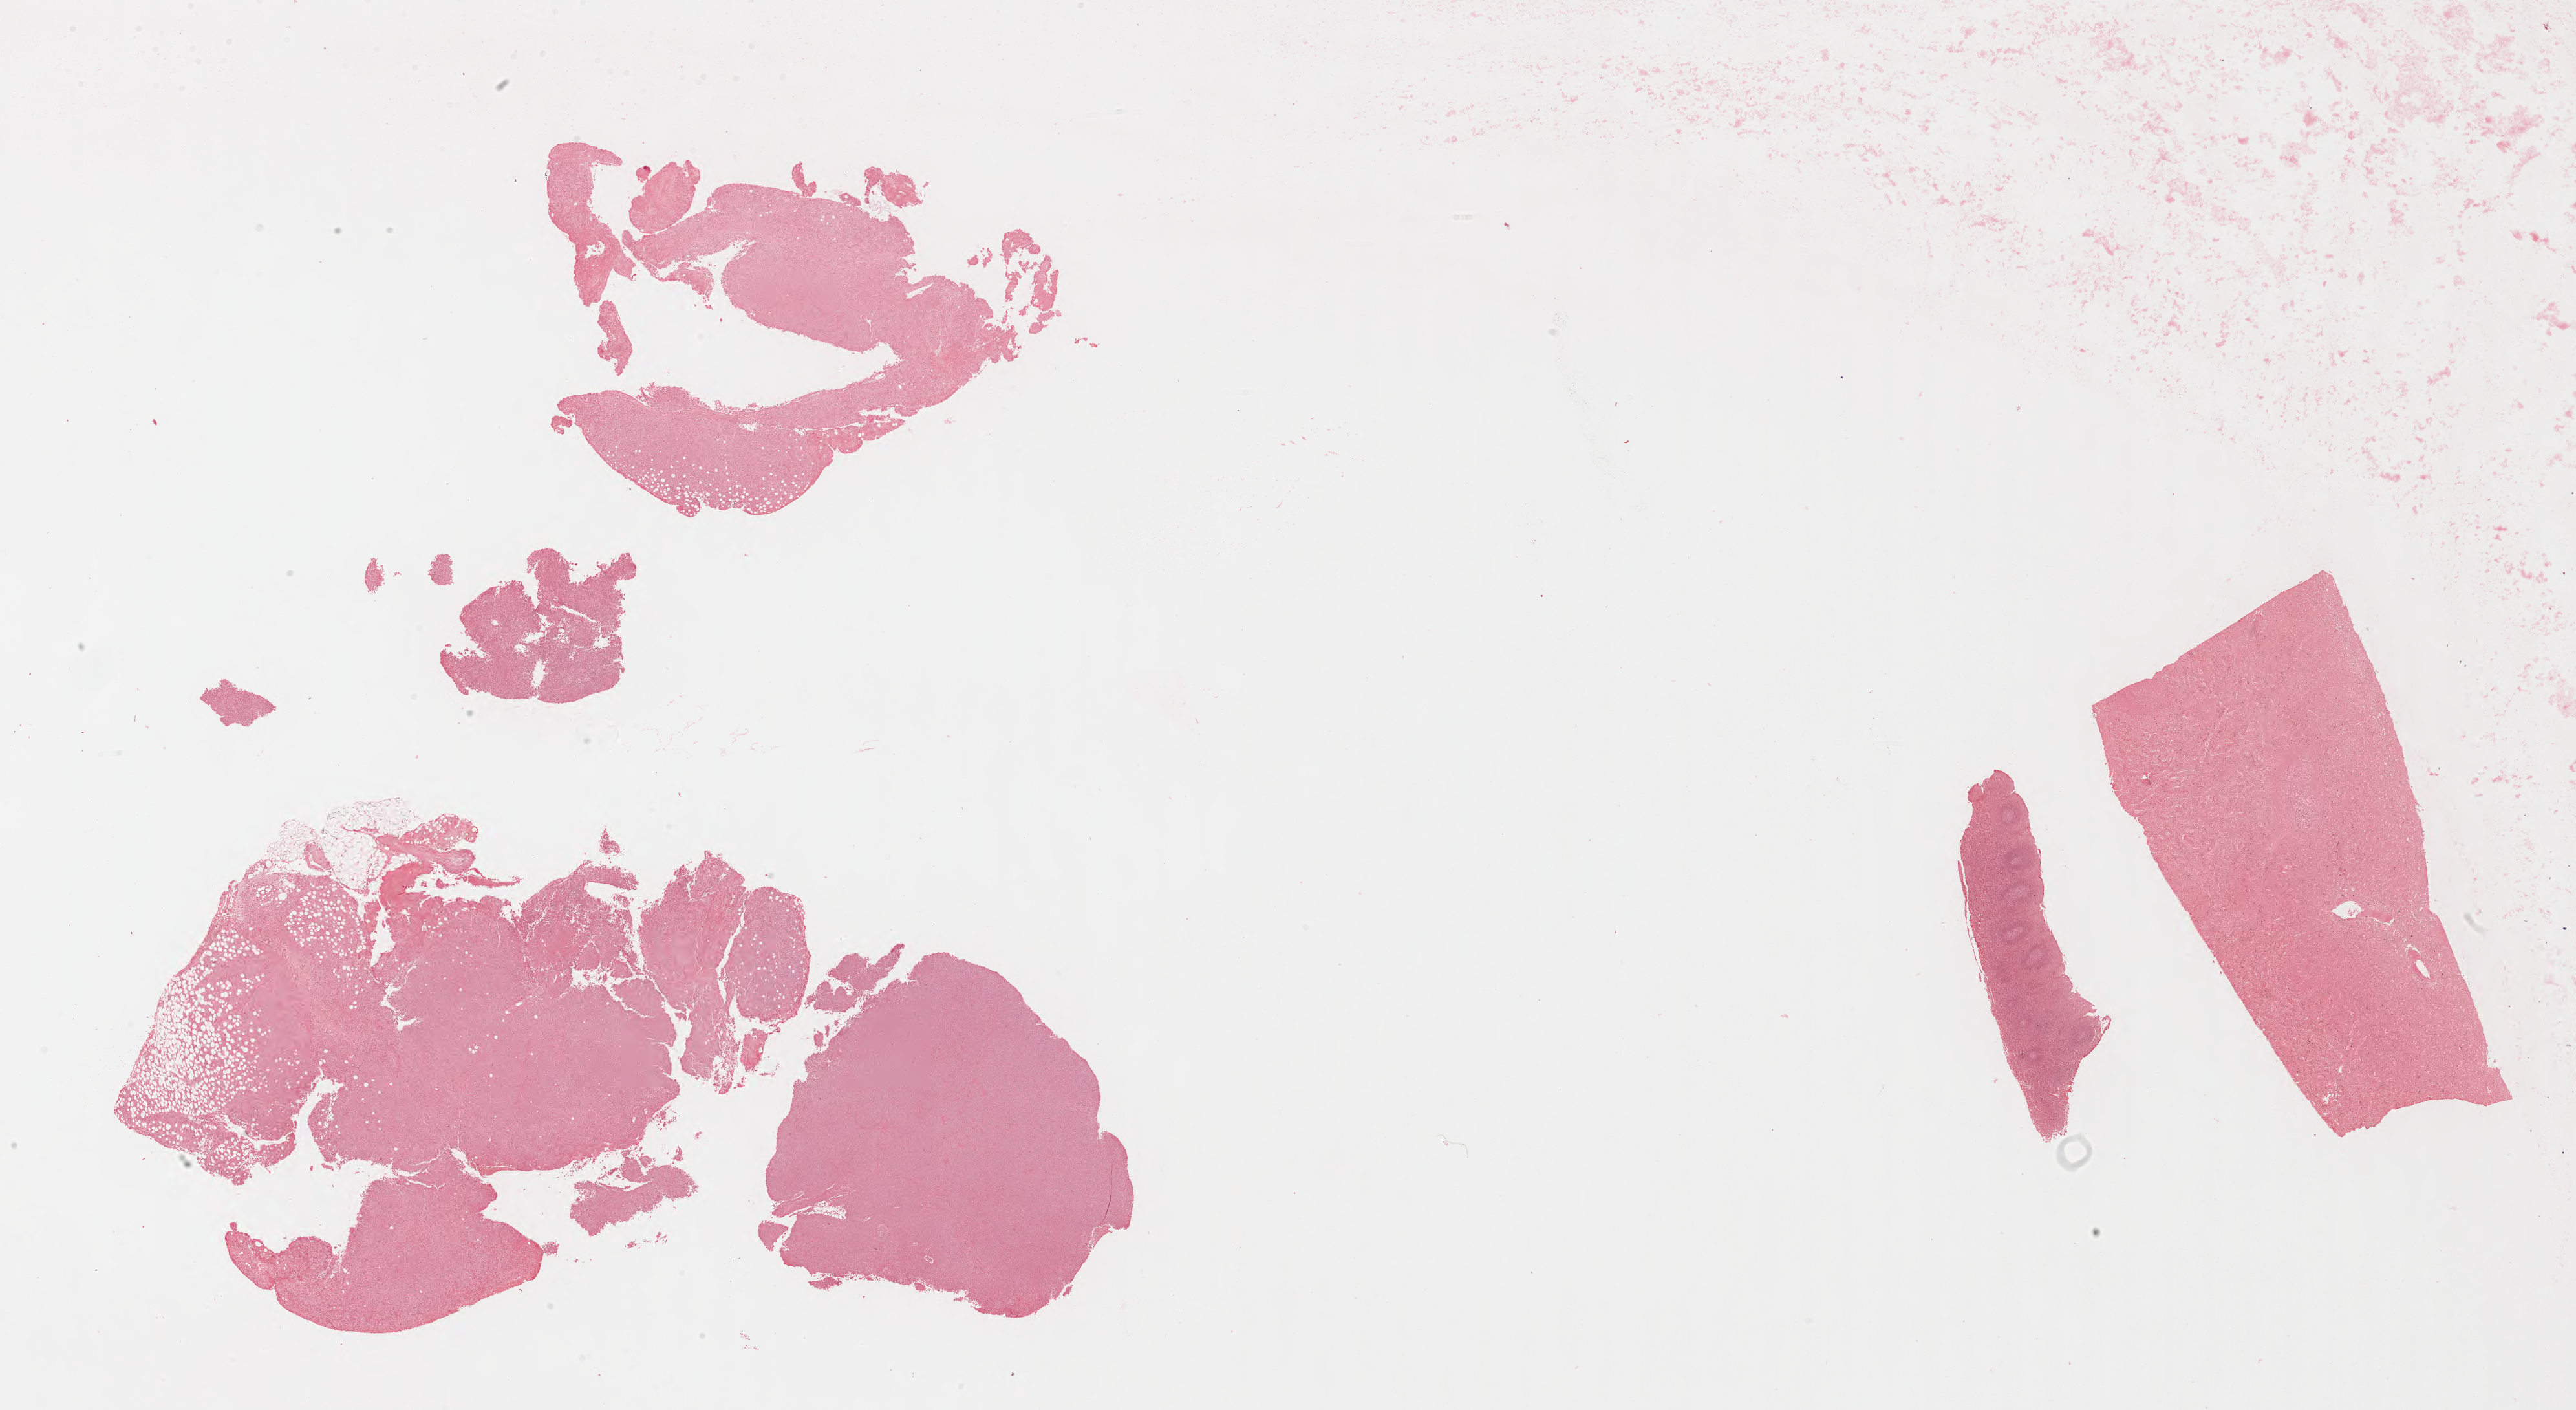
Whole-slide image, Epstein–Barr virus-encoded RNA (EBER) in-situ hybridisation, a low-resolution overview of the entire scanned area, about 32.2 x 17.6 mm. Specimen: tumor tissue. Female patient, aged 32.
Diagnosis: Diffuse large B-cell lymphoma, NOS.